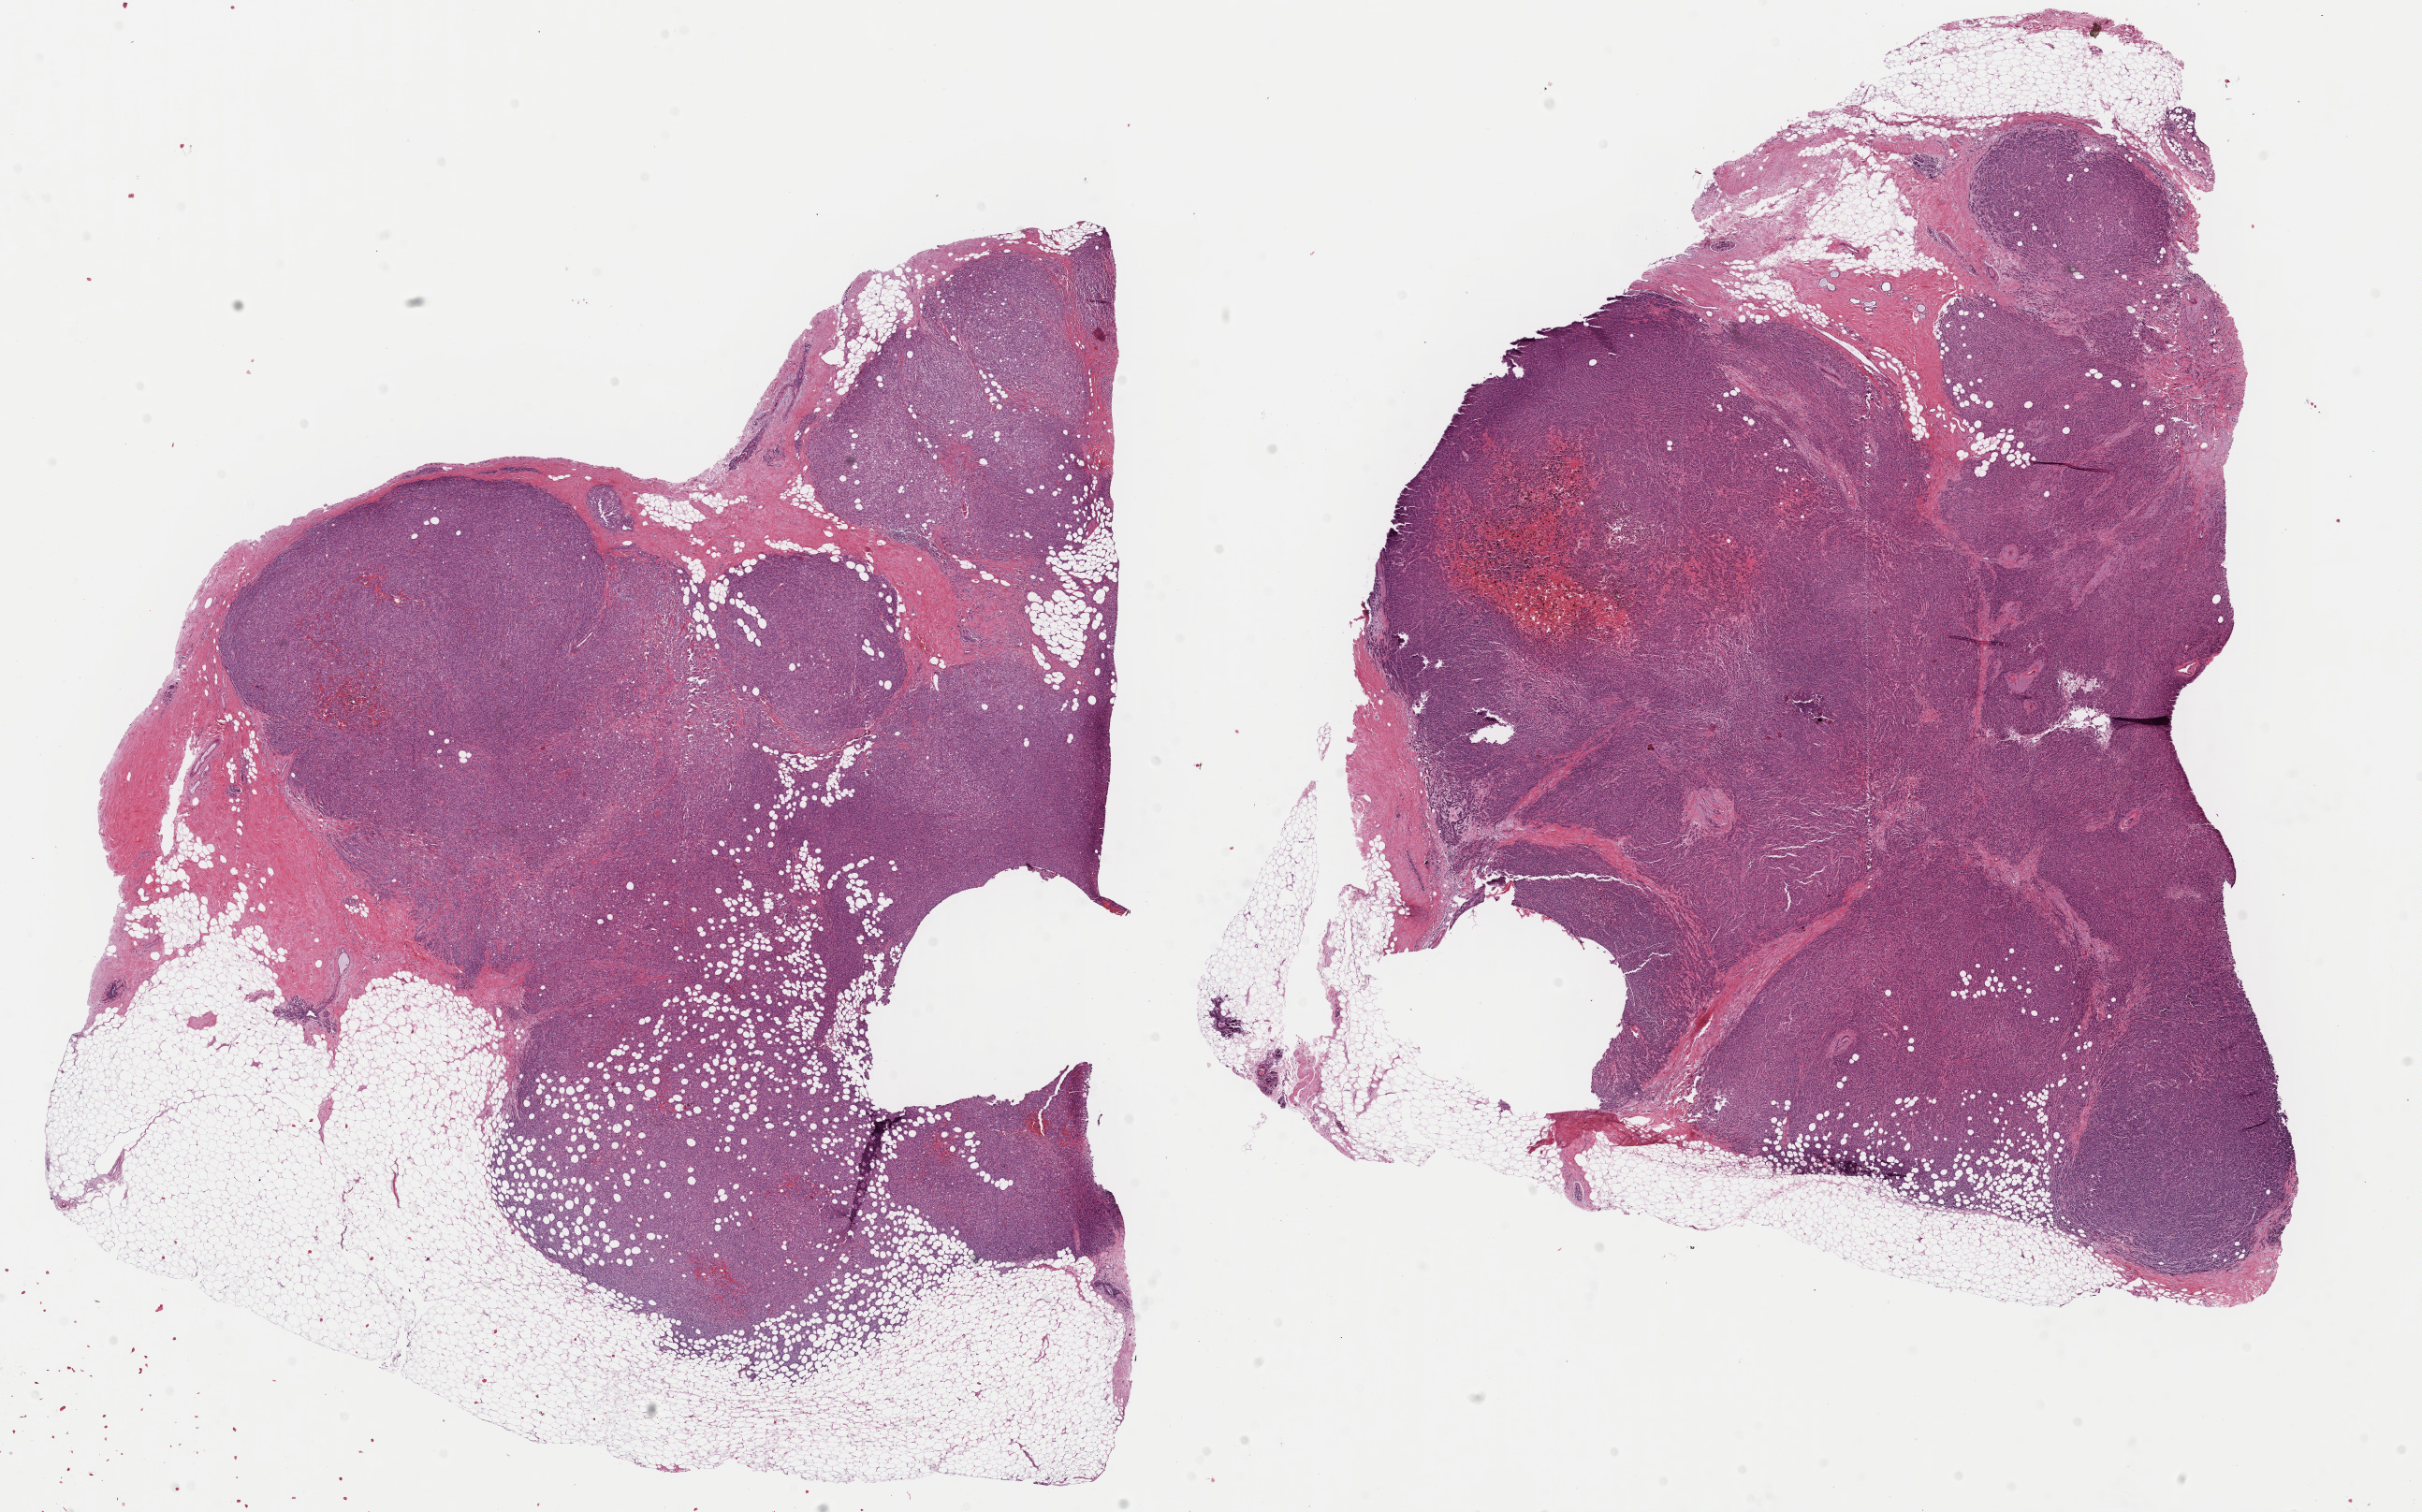
Digitized Hematoxylin and eosin (H&E) stained tissue section (whole slide) — low-resolution overview of the scanned area, about 20.4 x 12.8 mm (acquisition: 40x scan), formalin-fixed paraffin-embedded (FFPE) diagnostic section, primary tumour sample from the breast. Female patient; age at initial diagnosis 70 years.
Histologic diagnosis: Lobular carcinoma, NOS.